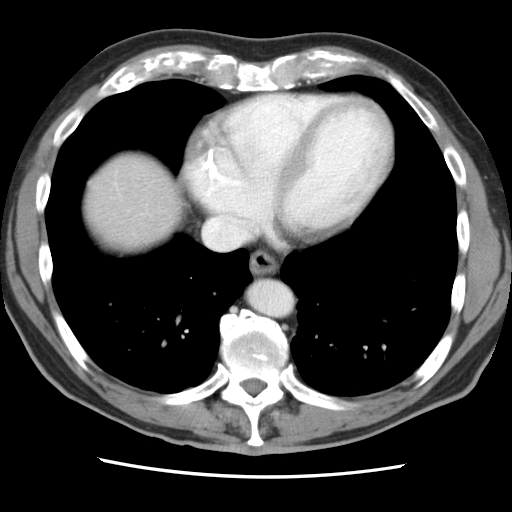
Contrast-enhanced abdominal CT, one axial slice; position 81 of 83 along the scan axis; 120 kVp; intravenous contrast given; soft-tissue window (W 400 / L 40 HU); 5 mm slice thickness; 512 × 512 image matrix, field of view 321 × 321 mm. Male patient, age 69 years. Case-level facts recorded for this patient, not image findings: diagnosis: colorectal cancer liver metastases, imaged before liver resection; multiple liver metastases: yes; largest metastasis: 3.5 cm; disease in both lobes: no.
Annotated regions visible in this slice (manually delineated by an expert):
- liver: bounding box <81,152,181,250> (left, top, right, bottom; pixels)
- planned liver remnant (the part of the liver to remain after resection): <81,157,181,250>